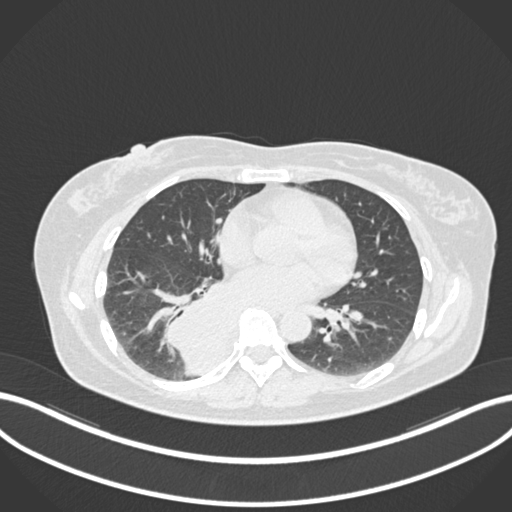
Chest CT, one axial slice. Position 574 of 677 along the scan axis. Reconstruction kernel B30f. Lung window (W 1500 / L -600 HU). 1 mm slice thickness. 512 × 512 image matrix, field of view 400 × 400 mm. Female patient, age 54 years. From the clinical record (not read from this slice): clinical TNM (as recorded): T4 N0 M0.
Outlined on this slice (bounding box drawn by a radiologist):
- lung tumour (recorded histology: adenocarcinoma): bounding box [x1, y1, x2, y2] px = [160, 284, 250, 378]